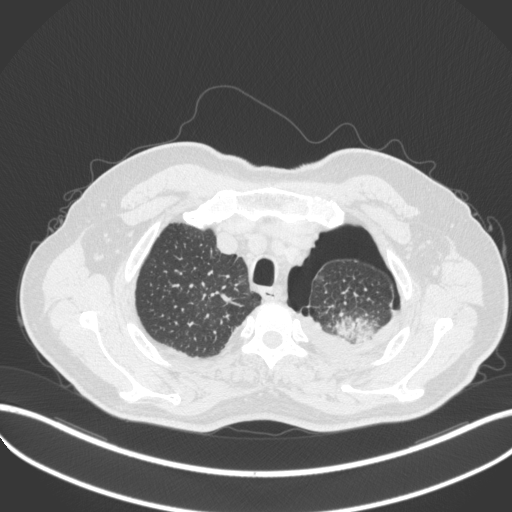
Chest CT, one axial slice. Position 421 of 466 along the scan axis. Lung window (W 1500 / L -600 HU). 512 × 512 image matrix, field of view 400 × 400 mm. Patient: male, 76 years. From the clinical record (not read from this slice): clinical TNM (as recorded): T3 N0 M1b.
Structures marked on this image (rectangle marked by the reading radiologist):
- lung tumour (recorded histology: adenocarcinoma): bounding box [x1, y1, x2, y2] px = [327, 311, 376, 345]